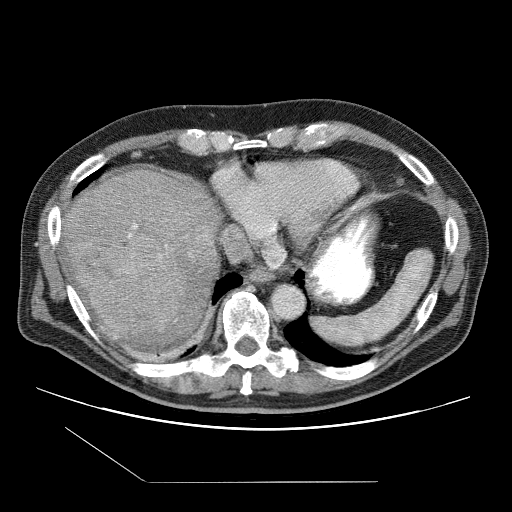
Contrast-enhanced abdominal CT (liver protocol), one axial slice. Position 88 of 109 along the scan axis. Reconstruction kernel STANDARD. One of 2 acquisitions stored at this slice position. Soft-tissue window (W 400 / L 40 HU). 2.5 mm slice thickness. 512 × 512 image matrix, field of view 400 × 400 mm. From the clinical record (not read from this slice): diagnosis: hepatocellular carcinoma (patient treated with transarterial chemoembolisation; whether this scan precedes or follows treatment is not stated here); TNM stage (as recorded): Stage-IIIB; Child-Pugh class: A; tumour nodularity: multinodular.
Outlined on this slice (semi-automatically segmented with operator editing):
- liver parenchyma outside the tumour (the mass and vessels are separate outlines, so this box may not span the whole liver): box from (x=60, y=170) to (x=222, y=340) px
- mass: (x=77, y=234)–(x=184, y=335)
- liver vessels: (x=128, y=225)–(x=167, y=247)